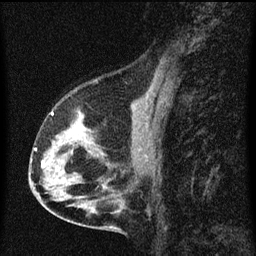
Breast MRI (dynamic contrast-enhanced), one sagittal slice; slice 33 of 60 in the series (ordered by position); dynamic contrast-enhanced series, image 2 of 3 at this slice position (ordered by acquisition); 1.5 T; TE 4.2 ms, TR 8 ms; 2 mm slice thickness; 256 × 256 image matrix, field of view 180 × 180 mm. Patient: female, 56 years.
Annotated regions visible in this slice (semi-automatic segmentation, software-assisted and operator-edited):
- analysis volume of interest (the breast-tissue region the enhancement analysis was run in; not a lesion): bounding box <34,114,102,181> (left, top, right, bottom; pixels)
- tumour enhancement mask (voxels above the 70 % enhancement threshold inside the analysis volume of interest): <34,148,45,168>